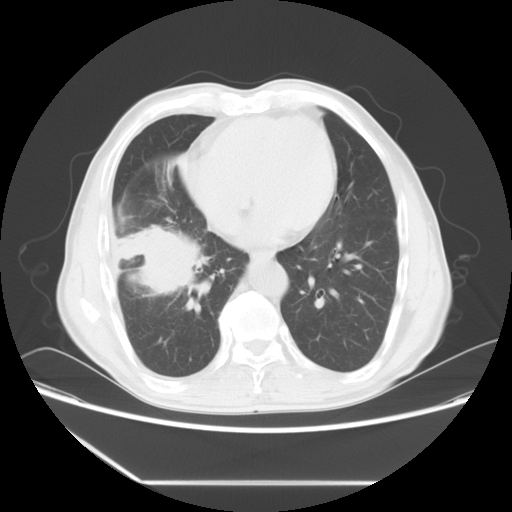
Chest CT, one axial slice; position 23 of 60 along the scan axis; 120 kVp; lung window (W 1500 / L -600 HU); 5 mm slice thickness; 512 × 512 image matrix. Patient: male, 72 years. Case-level facts recorded for this patient, not image findings: clinical TNM (as recorded): T1c N0 M0.
Outlined on this slice (rectangle marked by the reading radiologist):
- lung tumour (recorded histology: squamous cell carcinoma): box from (x=108, y=220) to (x=208, y=309) px